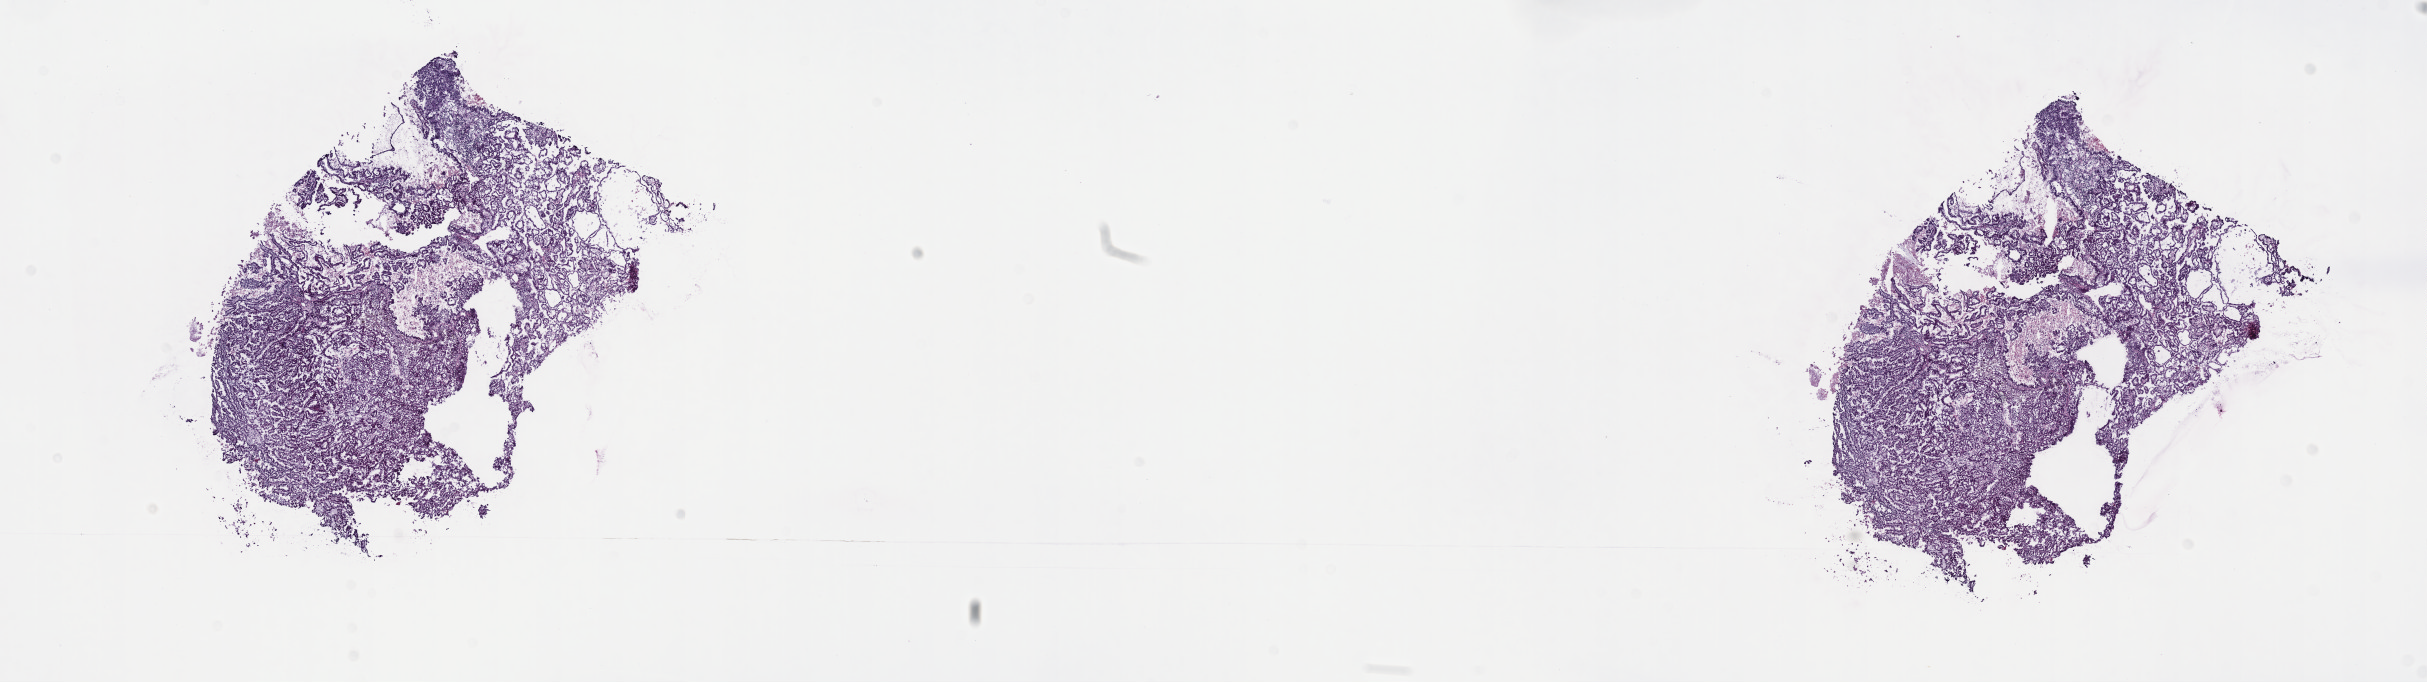
H&E-stained whole-slide image — whole scanned area (about 19.6 x 5.5 mm, from a 40x scan) shown as a low-resolution overview, frozen section from the top of the tissue portion, sample: primary tumour, kidney. Male patient; age at initial diagnosis 71 years. Pathologist review of this section (percent, as recorded): tumour cells 88%, tumour nuclei 90%, normal cells 0%, stromal cells 6%, necrosis 6%. Inflammatory infiltration, as recorded: lymphocyte infiltration 5%, monocyte infiltration 3%, neutrophil infiltration 1%.
• laterality: left
• AJCC pathologic stage: I
• histologic diagnosis: Papillary adenocarcinoma, NOS